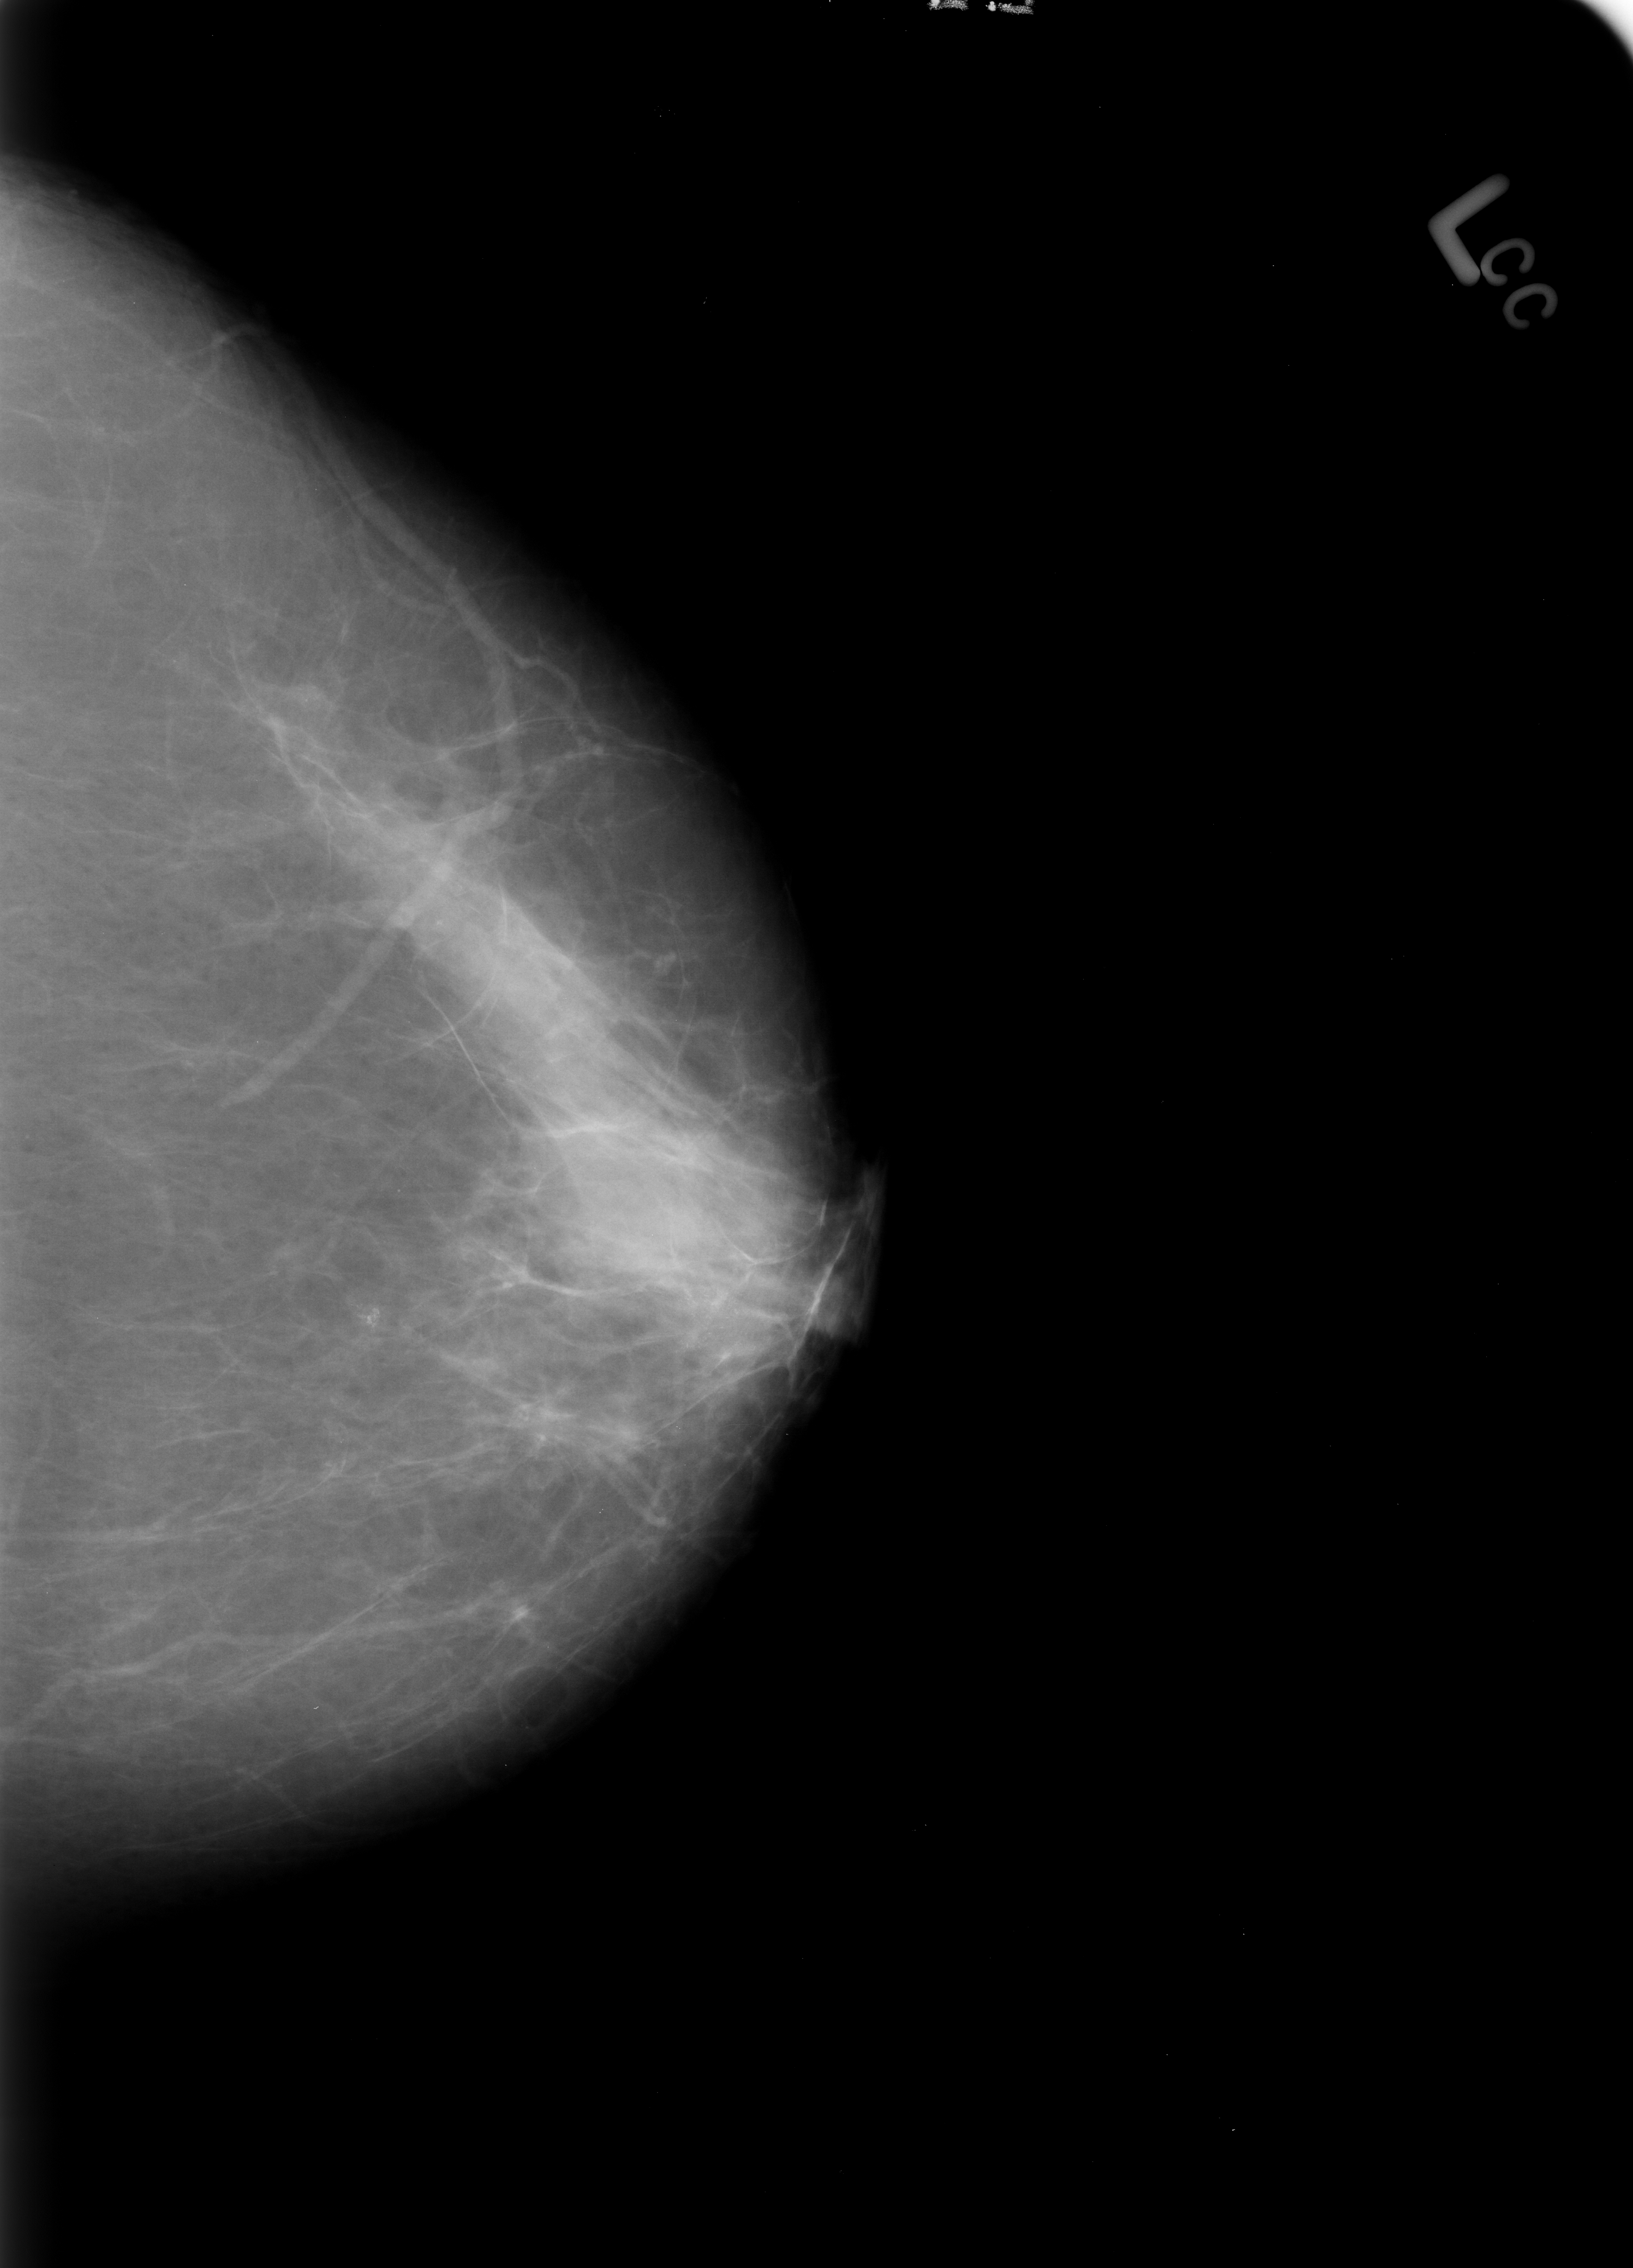
Digitized screen-film mammogram; left breast; CC view; BI-RADS breast density category 2 (scale 1–4).
Marked findings (only marked abnormalities are described; nothing is implied about the rest of the image): Finding 1 of 2: calcifications, morphology pleomorphic / fine linear branching, distribution clustered; BI-RADS assessment category 4; pathology (as recorded): benign. Finding 2 of 2: calcifications, morphology pleomorphic, distribution clustered; BI-RADS assessment category 4; pathology result (as recorded, not read from the image): benign.